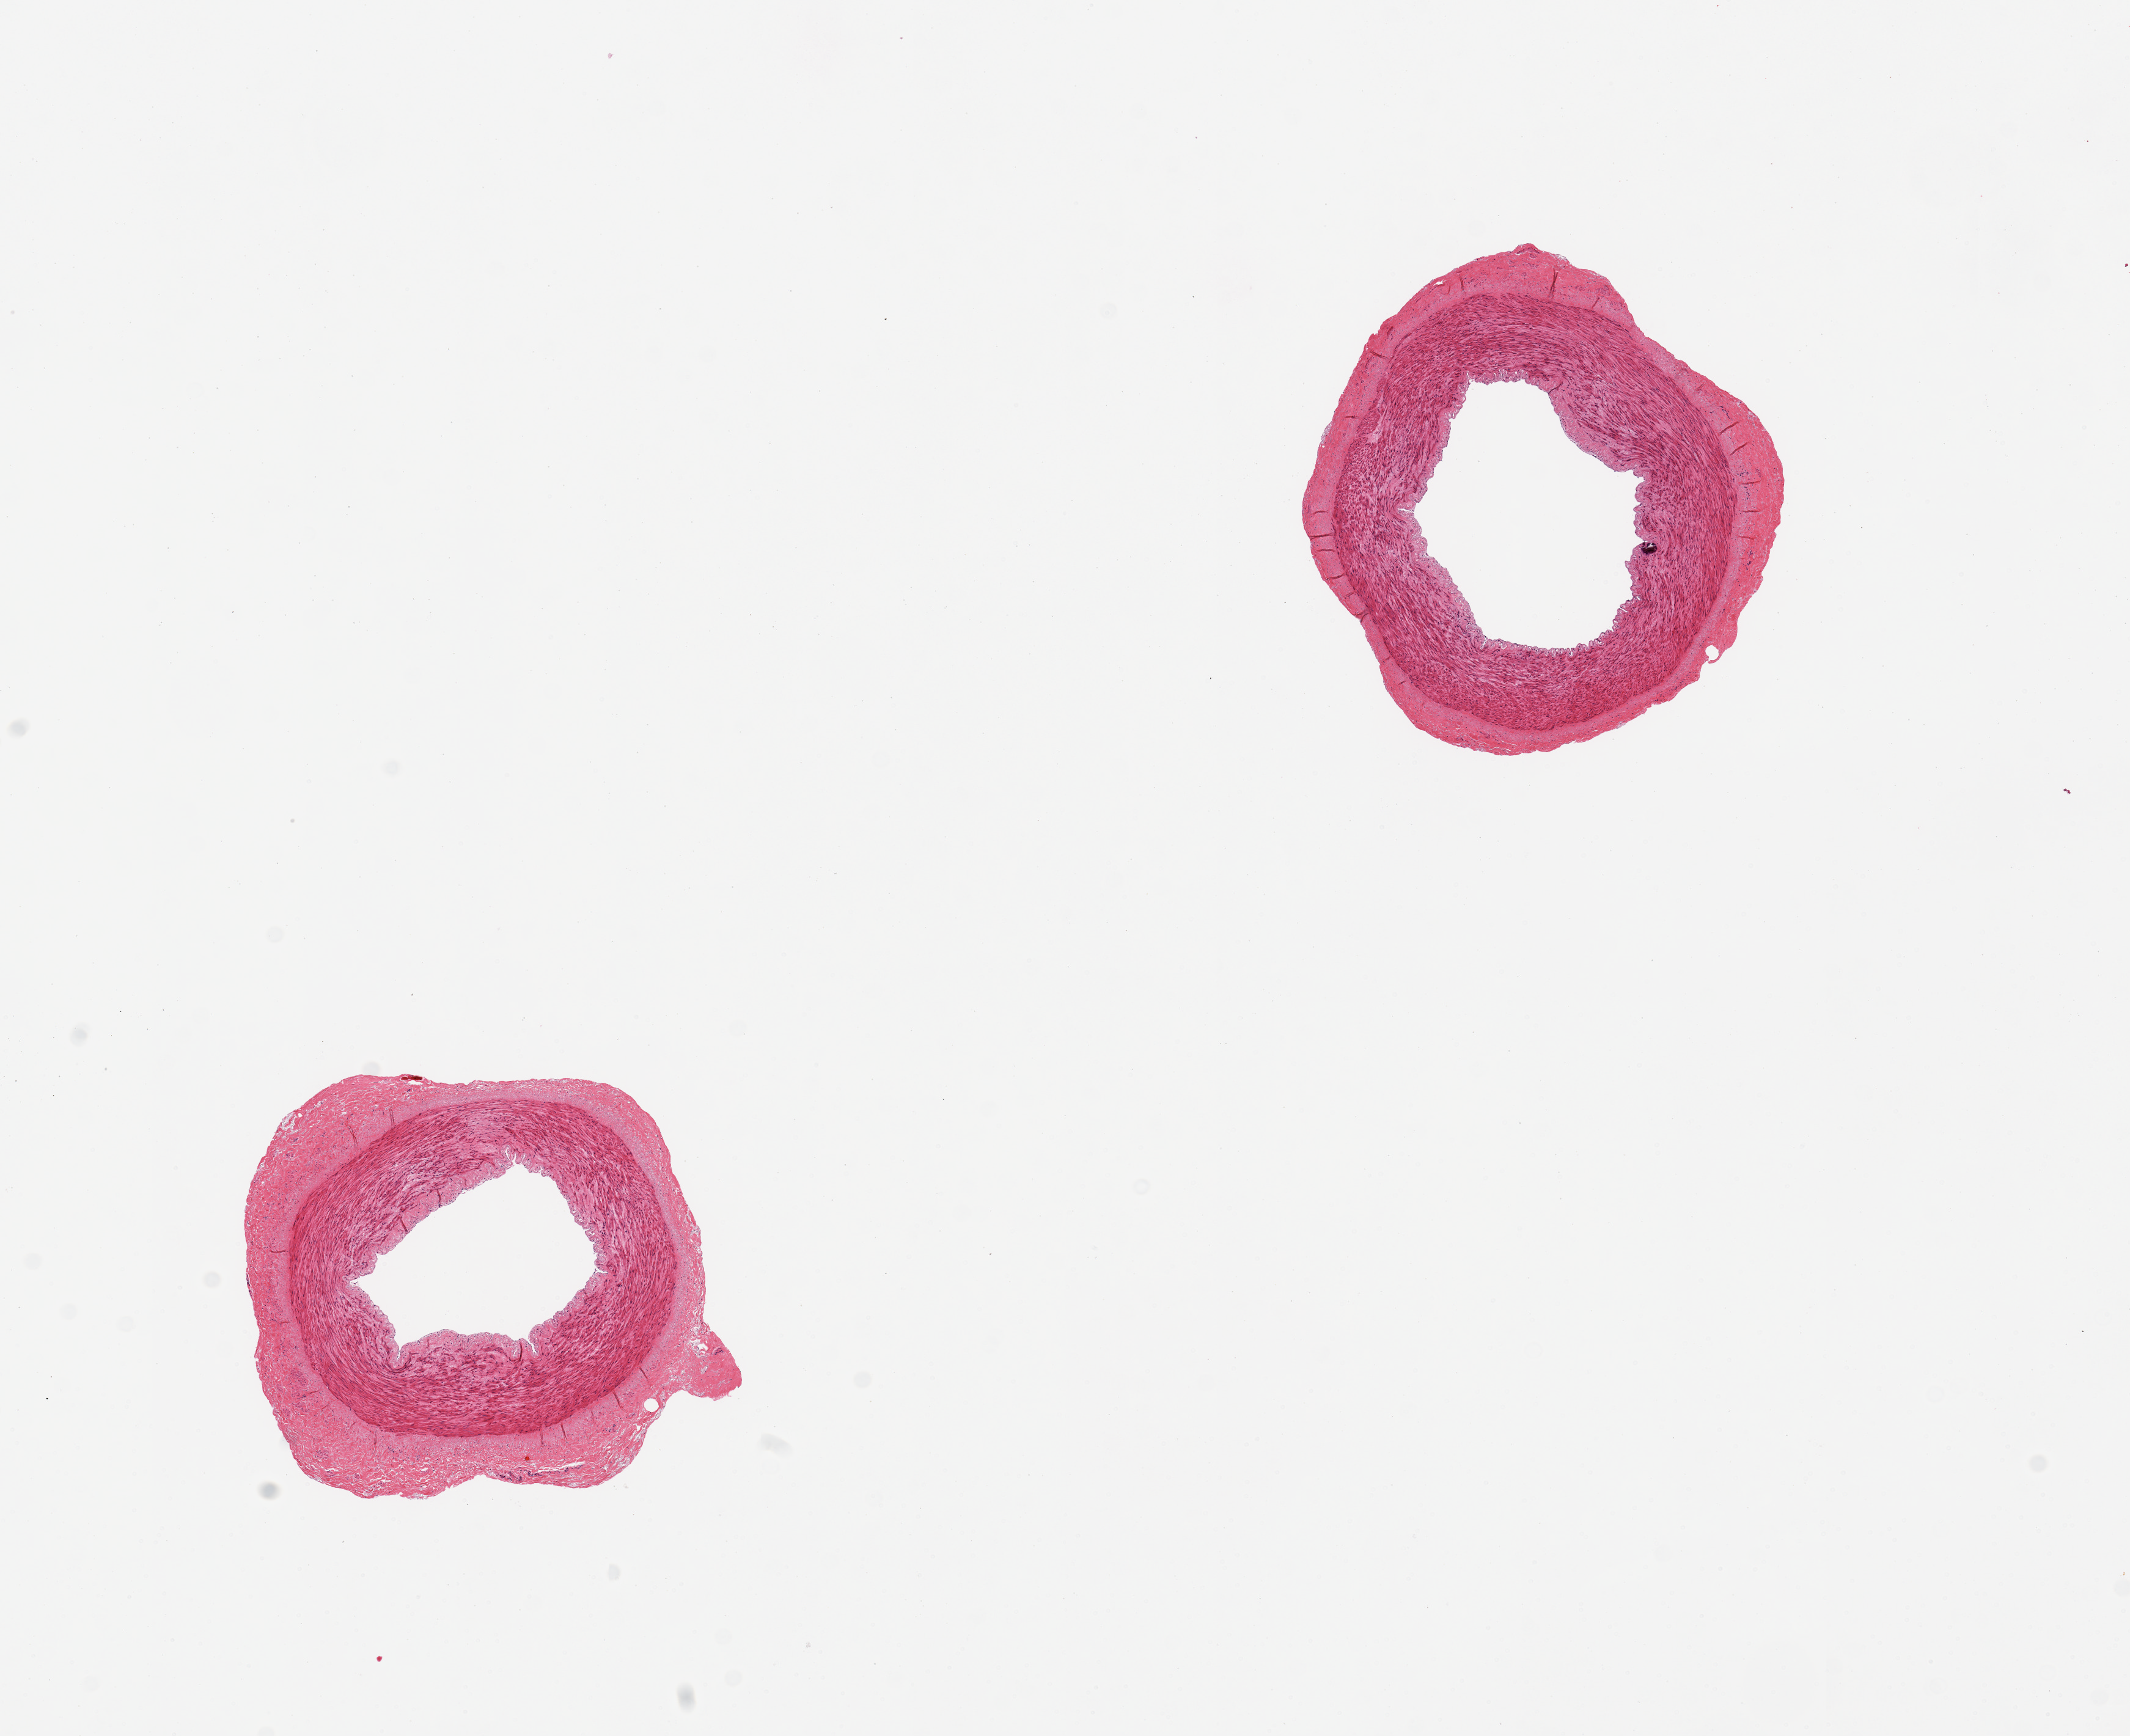
Whole-slide image, H&E stain — whole scanned area (about 13.8 x 11.2 mm, acquisition: 20x scan) shown as a low-resolution overview. PAXgene-fixed paraffin-embedded (PFPE) section. Sampled site (target tissue): tibial artery. Donor tissue sample.
- pathologist's review note for this sample: 2 pieces, minimal circumferential fibrous tissue up to ~0.3mm, good specimens